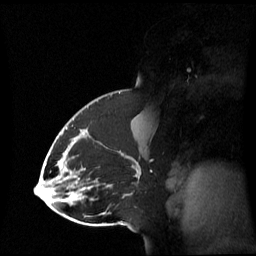
Breast MRI (dynamic contrast-enhanced), one sagittal slice. Position 37 of 60 along the scan axis. Dynamic contrast-enhanced series, image 2 of 3 at this slice position (ordered by acquisition). 1.5 T. TE 4.2 ms, TR 8.4 ms. 2.8 mm slice thickness. 256 × 256 image matrix, field of view 270 × 270 mm. Female patient, age 43 years. From the clinical record (not read from this slice): setting: breast cancer imaged before/during neoadjuvant chemotherapy; receptor status: triple-negative.
Structures marked on this image (semi-automatic segmentation, software-assisted and operator-edited):
- analysis volume of interest (the breast-tissue region the enhancement analysis was run in; not a lesion): bounding box <65,118,143,198> (left, top, right, bottom; pixels)
- tumour enhancement mask (voxels above the 70 % enhancement threshold inside the analysis volume of interest): <66,127,127,185>